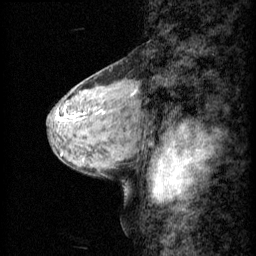
Breast MRI (dynamic contrast-enhanced), one sagittal slice; position 24 of 60 along the scan axis; 3 images stored at this slice position (order not interpretable as contrast timing); 1.5 T; TE 4.2 ms, TR 11 ms; 1.5 mm slice thickness; 256 × 256 image matrix, field of view 200 × 200 mm. Female patient, age 48 years.
Structures marked on this image (semi-automatic segmentation, software-assisted and operator-edited):
- analysis volume of interest (the breast-tissue region the enhancement analysis was run in; not a lesion): box from (x=61, y=76) to (x=140, y=143) px
- tumour enhancement mask (voxels above the 70 % enhancement threshold inside the analysis volume of interest): (x=132, y=90)–(x=136, y=95)